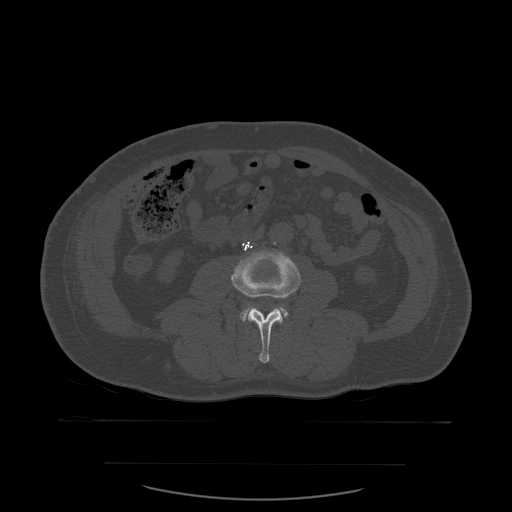
CT including the spine, one axial slice. Slice 185 of 590 in the series (ordered by position). Bone window (W 1800 / L 400 HU). 1.25 mm slice thickness. 512 × 512 image matrix, field of view 479 × 479 mm. Patient age 71 years. From the clinical record (not read from this slice): primary cancer: lung; vertebrae with lytic lesions (as recorded): T1, T2, L5, S1.
Outlined on this slice (semi-automatically segmented with operator editing):
- L3 vertebra: bounding box [x1, y1, x2, y2] px = [231, 250, 301, 364]
- L4 vertebra: [241, 305, 288, 322]